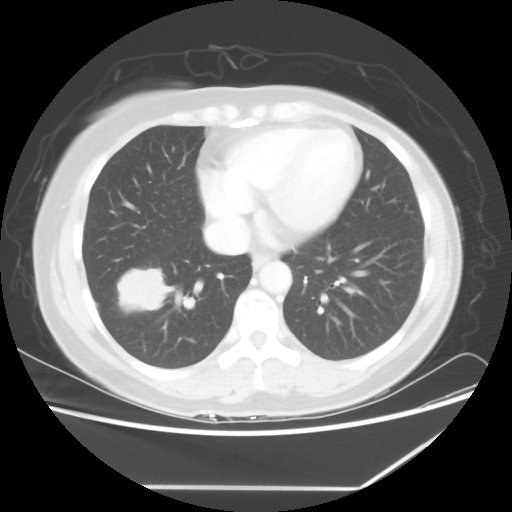
Chest CT, one axial slice; slice 23 of 60 in the series (ordered by position); 100 kVp; lung window (W 1500 / L -600 HU); 5 mm slice thickness; 512 × 512 image matrix, field of view 374 × 374 mm. Patient: female, 42 years. Case-level facts recorded for this patient, not image findings: clinical TNM (as recorded): T2 N1 M0.
Outlined on this slice (bounding box drawn by a radiologist):
- lung tumour (recorded histology: adenocarcinoma): box from (x=111, y=256) to (x=170, y=316) px